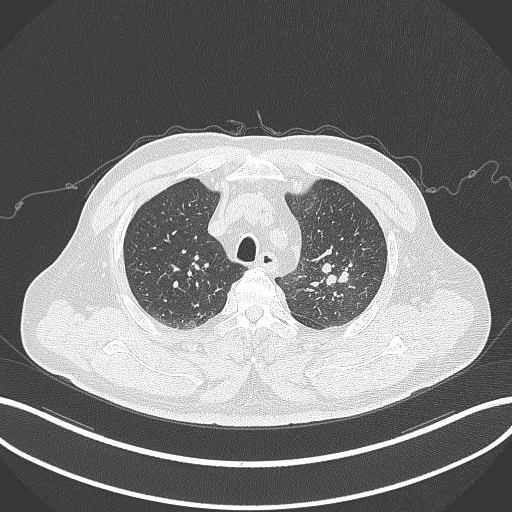
Chest CT, one axial slice. Slice 242 of 286 in the series (ordered by position). 120 kVp. Lung window (W 1500 / L -600 HU). 1 mm slice thickness. 512 × 512 image matrix, field of view 400 × 400 mm. Male patient, age 67 years. From the clinical record (not read from this slice): clinical TNM (as recorded): T2a N1 M0; histopathological grade: G3.
Annotated regions visible in this slice (rectangle marked by the reading radiologist):
- lung tumour (recorded histology: adenocarcinoma): box from (x=319, y=261) to (x=351, y=288) px